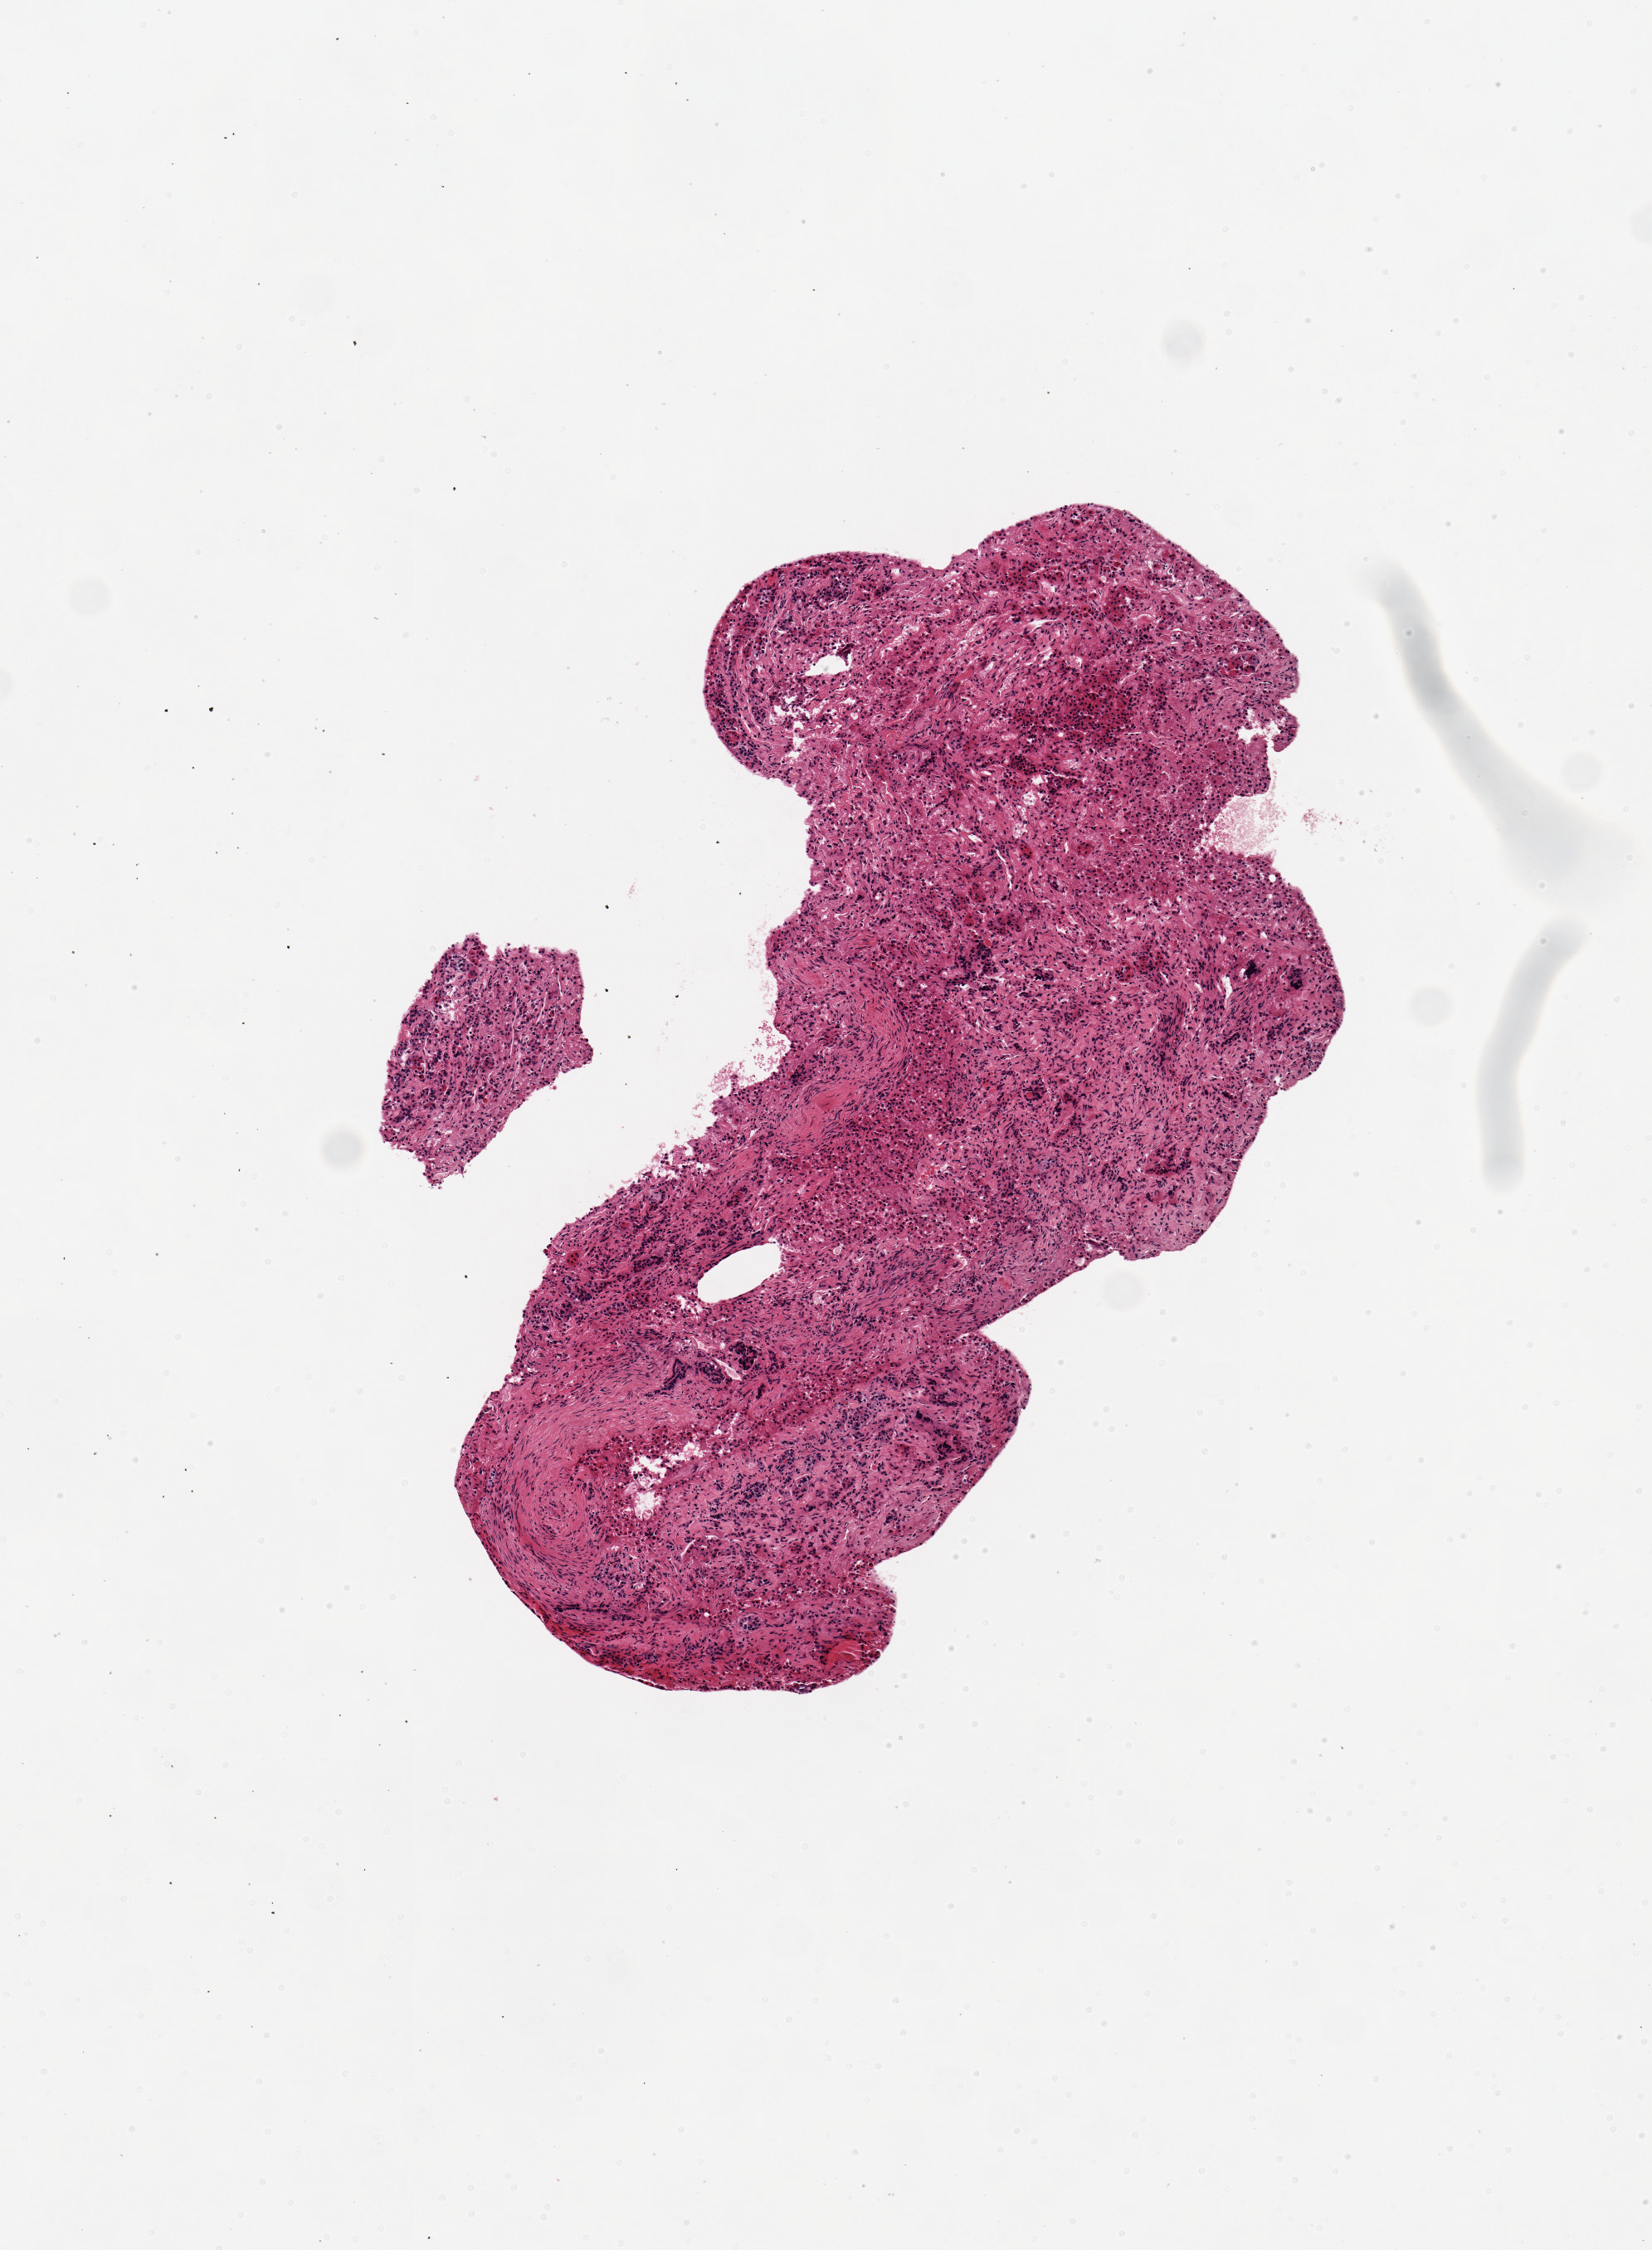
Digitized H&E-stained section, brightfield — a low-resolution overview of the entire scanned area, about 3.9 x 5.4 mm (from a 20x scan), PAXgene-fixed paraffin-embedded (PFPE) section, target tissue: pituitary, tissue donor sample. Donor: male.
* review note (as recorded): 2 pieces